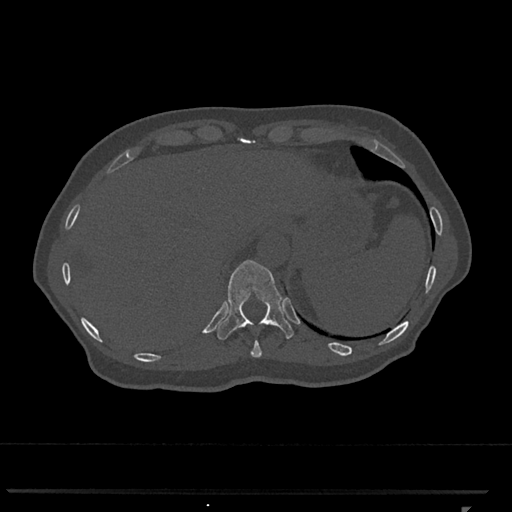
CT including the spine, one axial slice. Position 530 of 793 along the scan axis. 120 kVp. Bone window (W 1800 / L 400 HU). 0.5 mm slice thickness. 512 × 512 image matrix. Patient: female, 62 years. Case-level facts recorded for this patient, not image findings: primary cancer: renal.
Structures marked on this image (semi-automatic segmentation, software-assisted and operator-edited):
- T10 vertebra: bounding box <250,341,262,357> (left, top, right, bottom; pixels)
- T11 vertebra: <217,260,294,340>